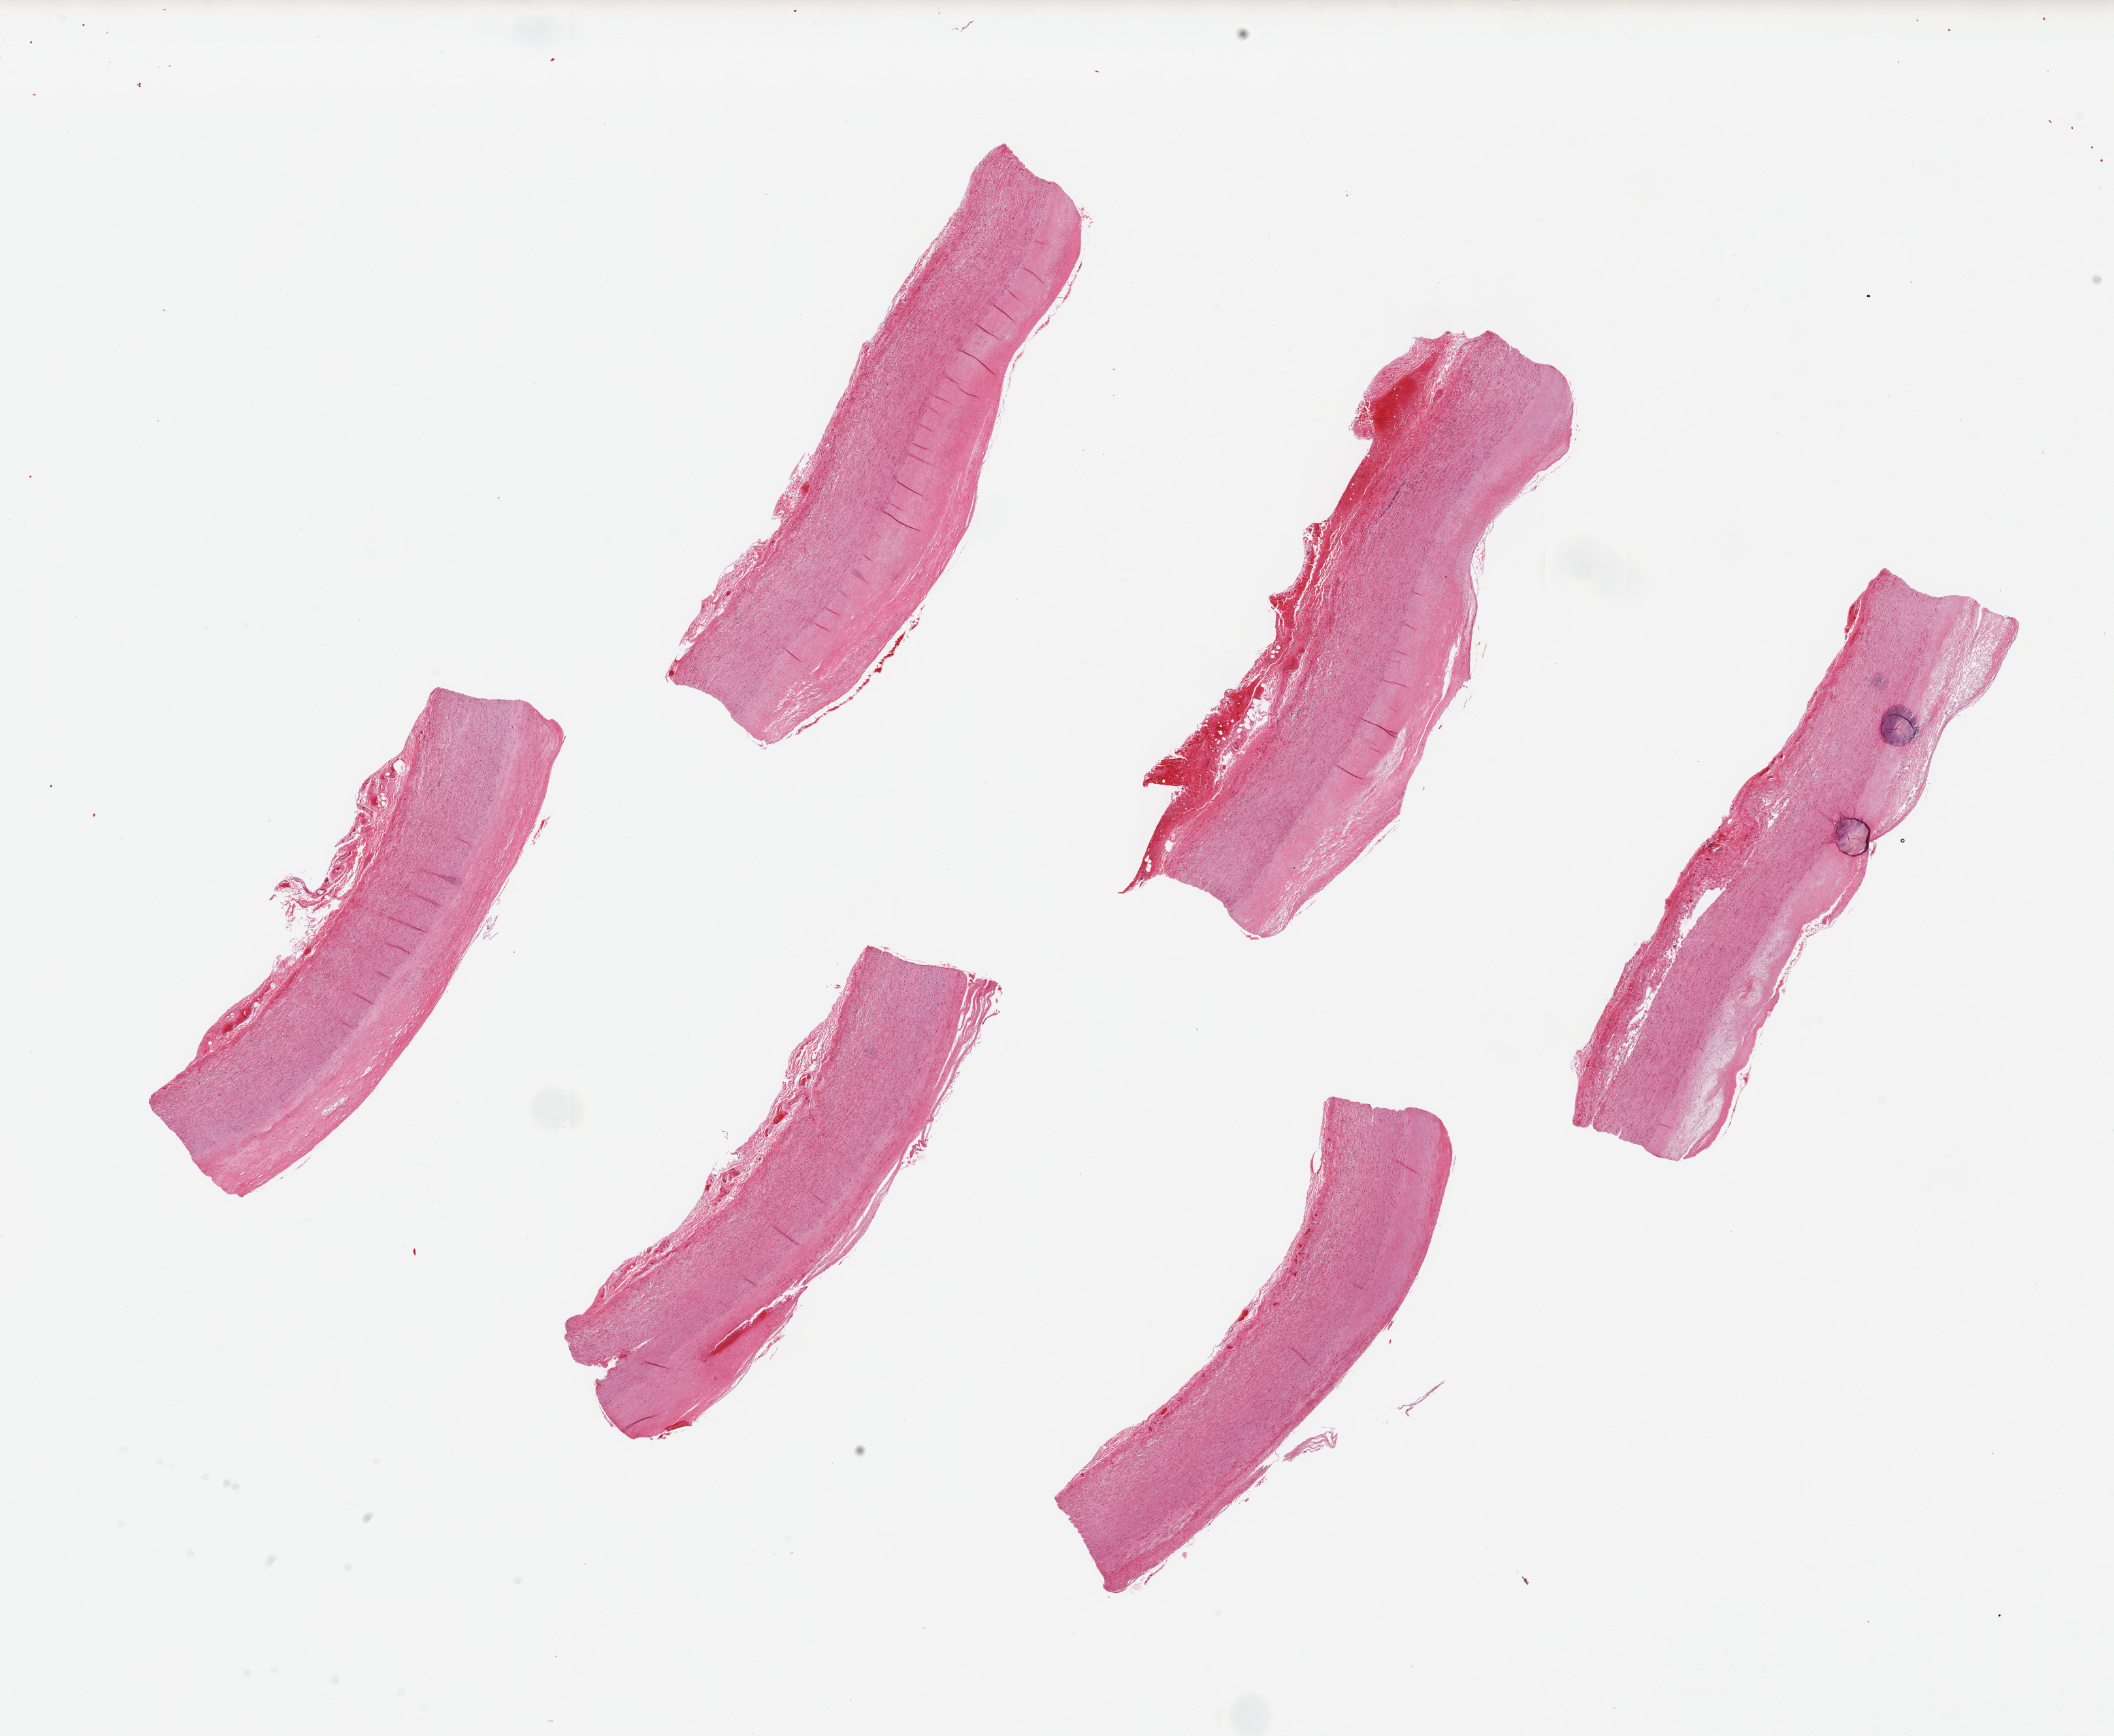
Haematoxylin and eosin whole-slide image, whole scanned area (about 25.6 x 21.0 mm) shown as a low-resolution overview. PAXgene-fixed, paraffin-embedded tissue. Sampled site (target tissue): aorta. Donor tissue sample.
* pathologist's review note for this sample: 6 pieces 7.5x1.5mm